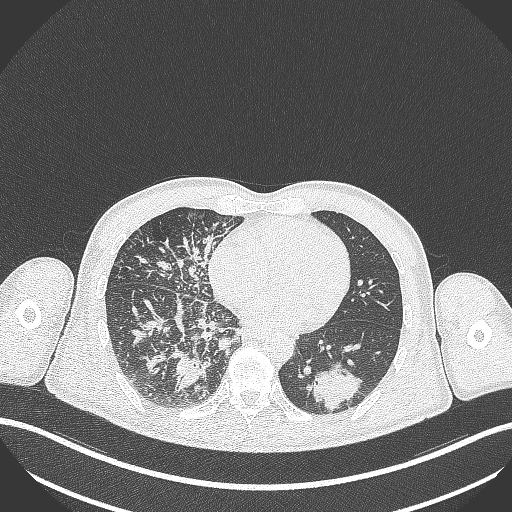
Chest CT, one axial slice; slice 116 of 348 in the series (ordered by position); reconstruction kernel B70f; 120 kVp; lung window (W 1500 / L -600 HU); 1 mm slice thickness; 512 × 512 image matrix. Patient: male, 49 years. Case-level facts recorded for this patient, not image findings: clinical TNM (as recorded): T2b N1 M0.
Structures marked on this image (bounding box drawn by a radiologist):
- lung tumour (recorded histology: adenocarcinoma): box from (x=299, y=363) to (x=365, y=412) px